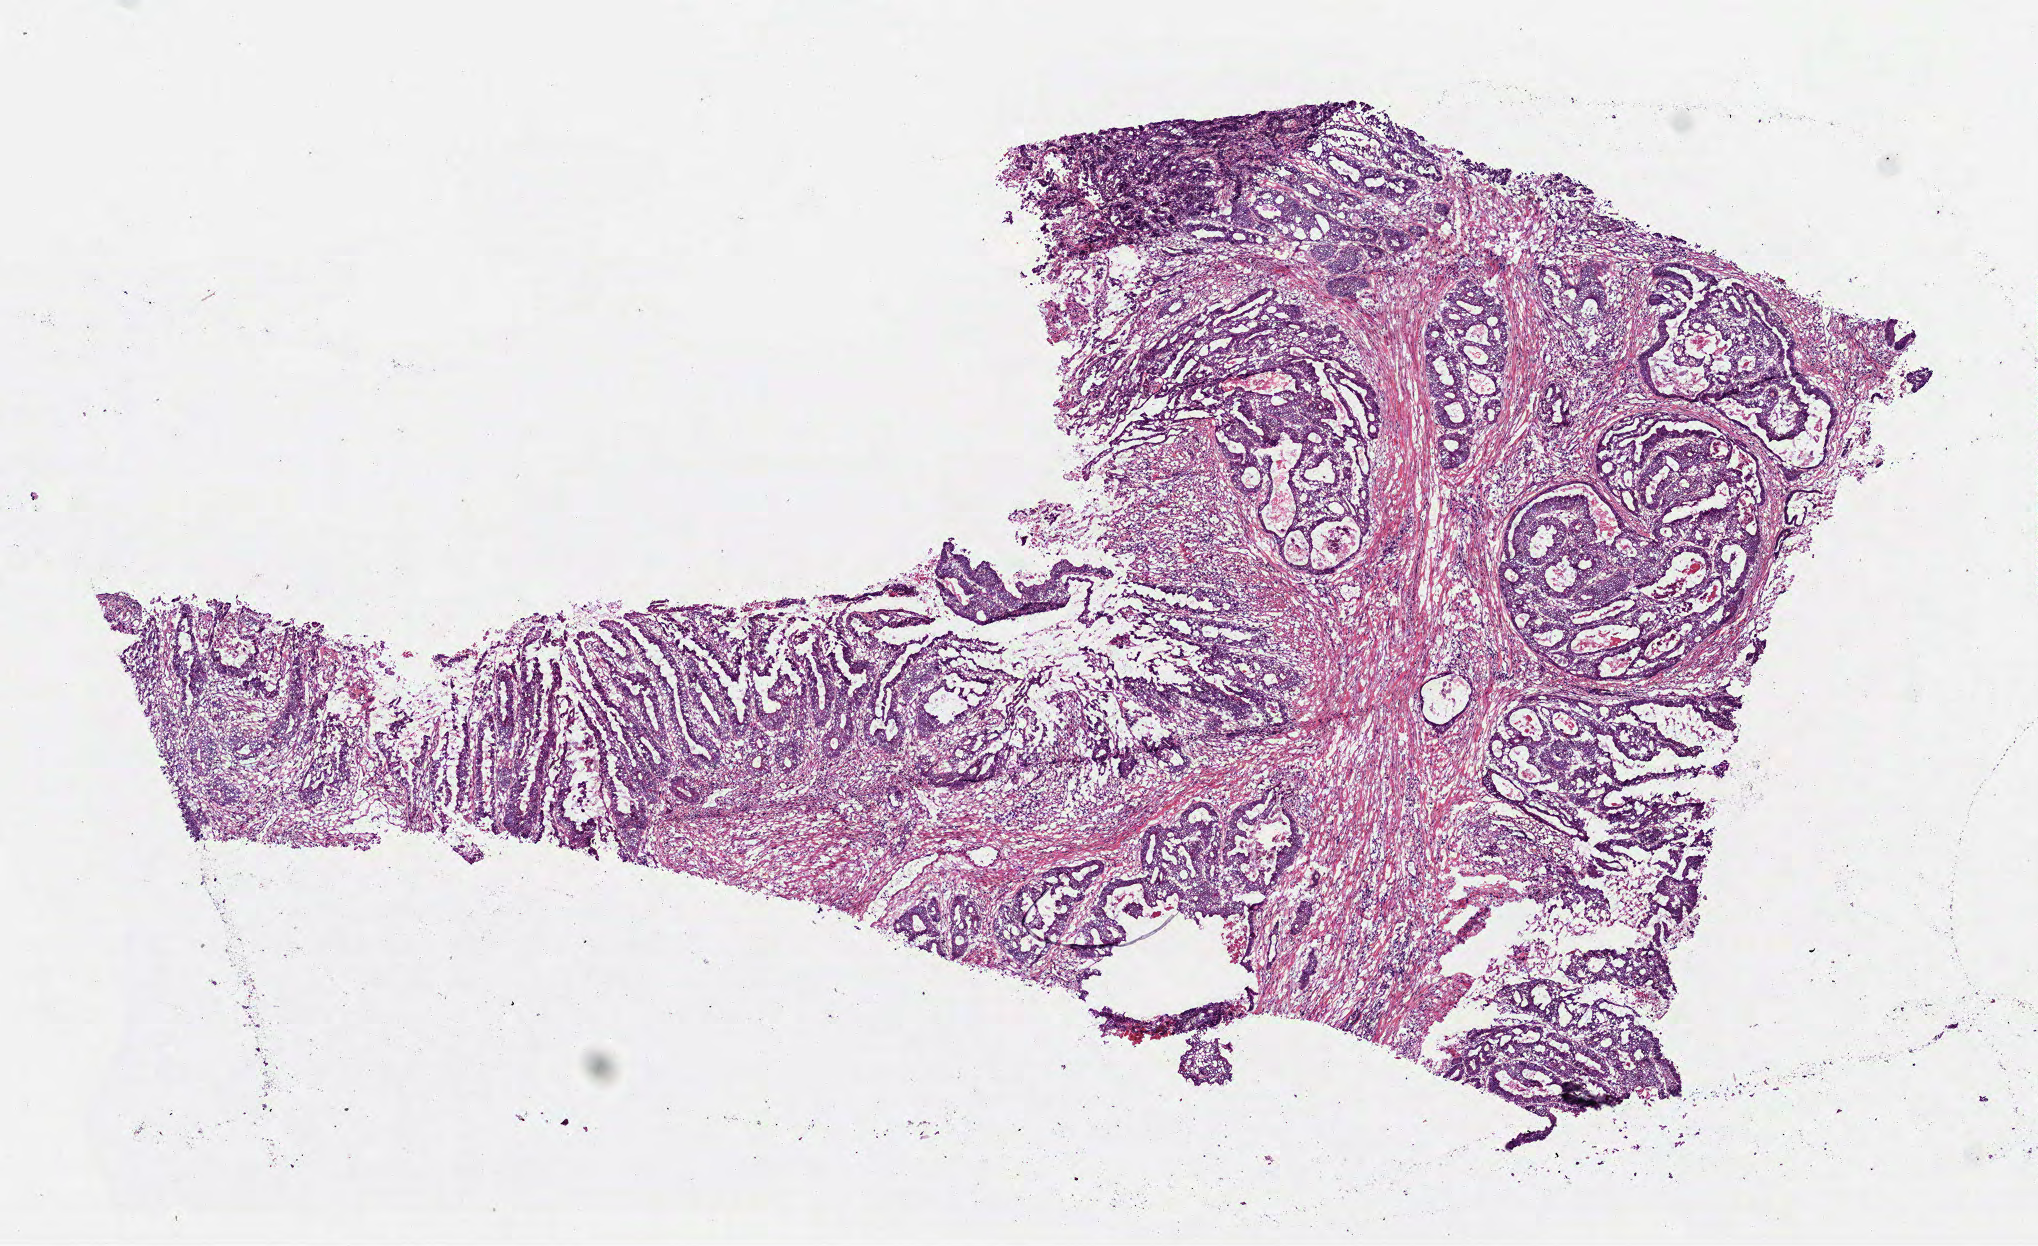
H&E-stained whole-slide image — shown as a low-resolution overview of the whole scanned area (about 8.2 x 5.0 mm, acquisition: 40x scan); frozen section; sample: primary tumour, rectum. Female patient.
Pathologic diagnosis: Adenocarcinoma, NOS.